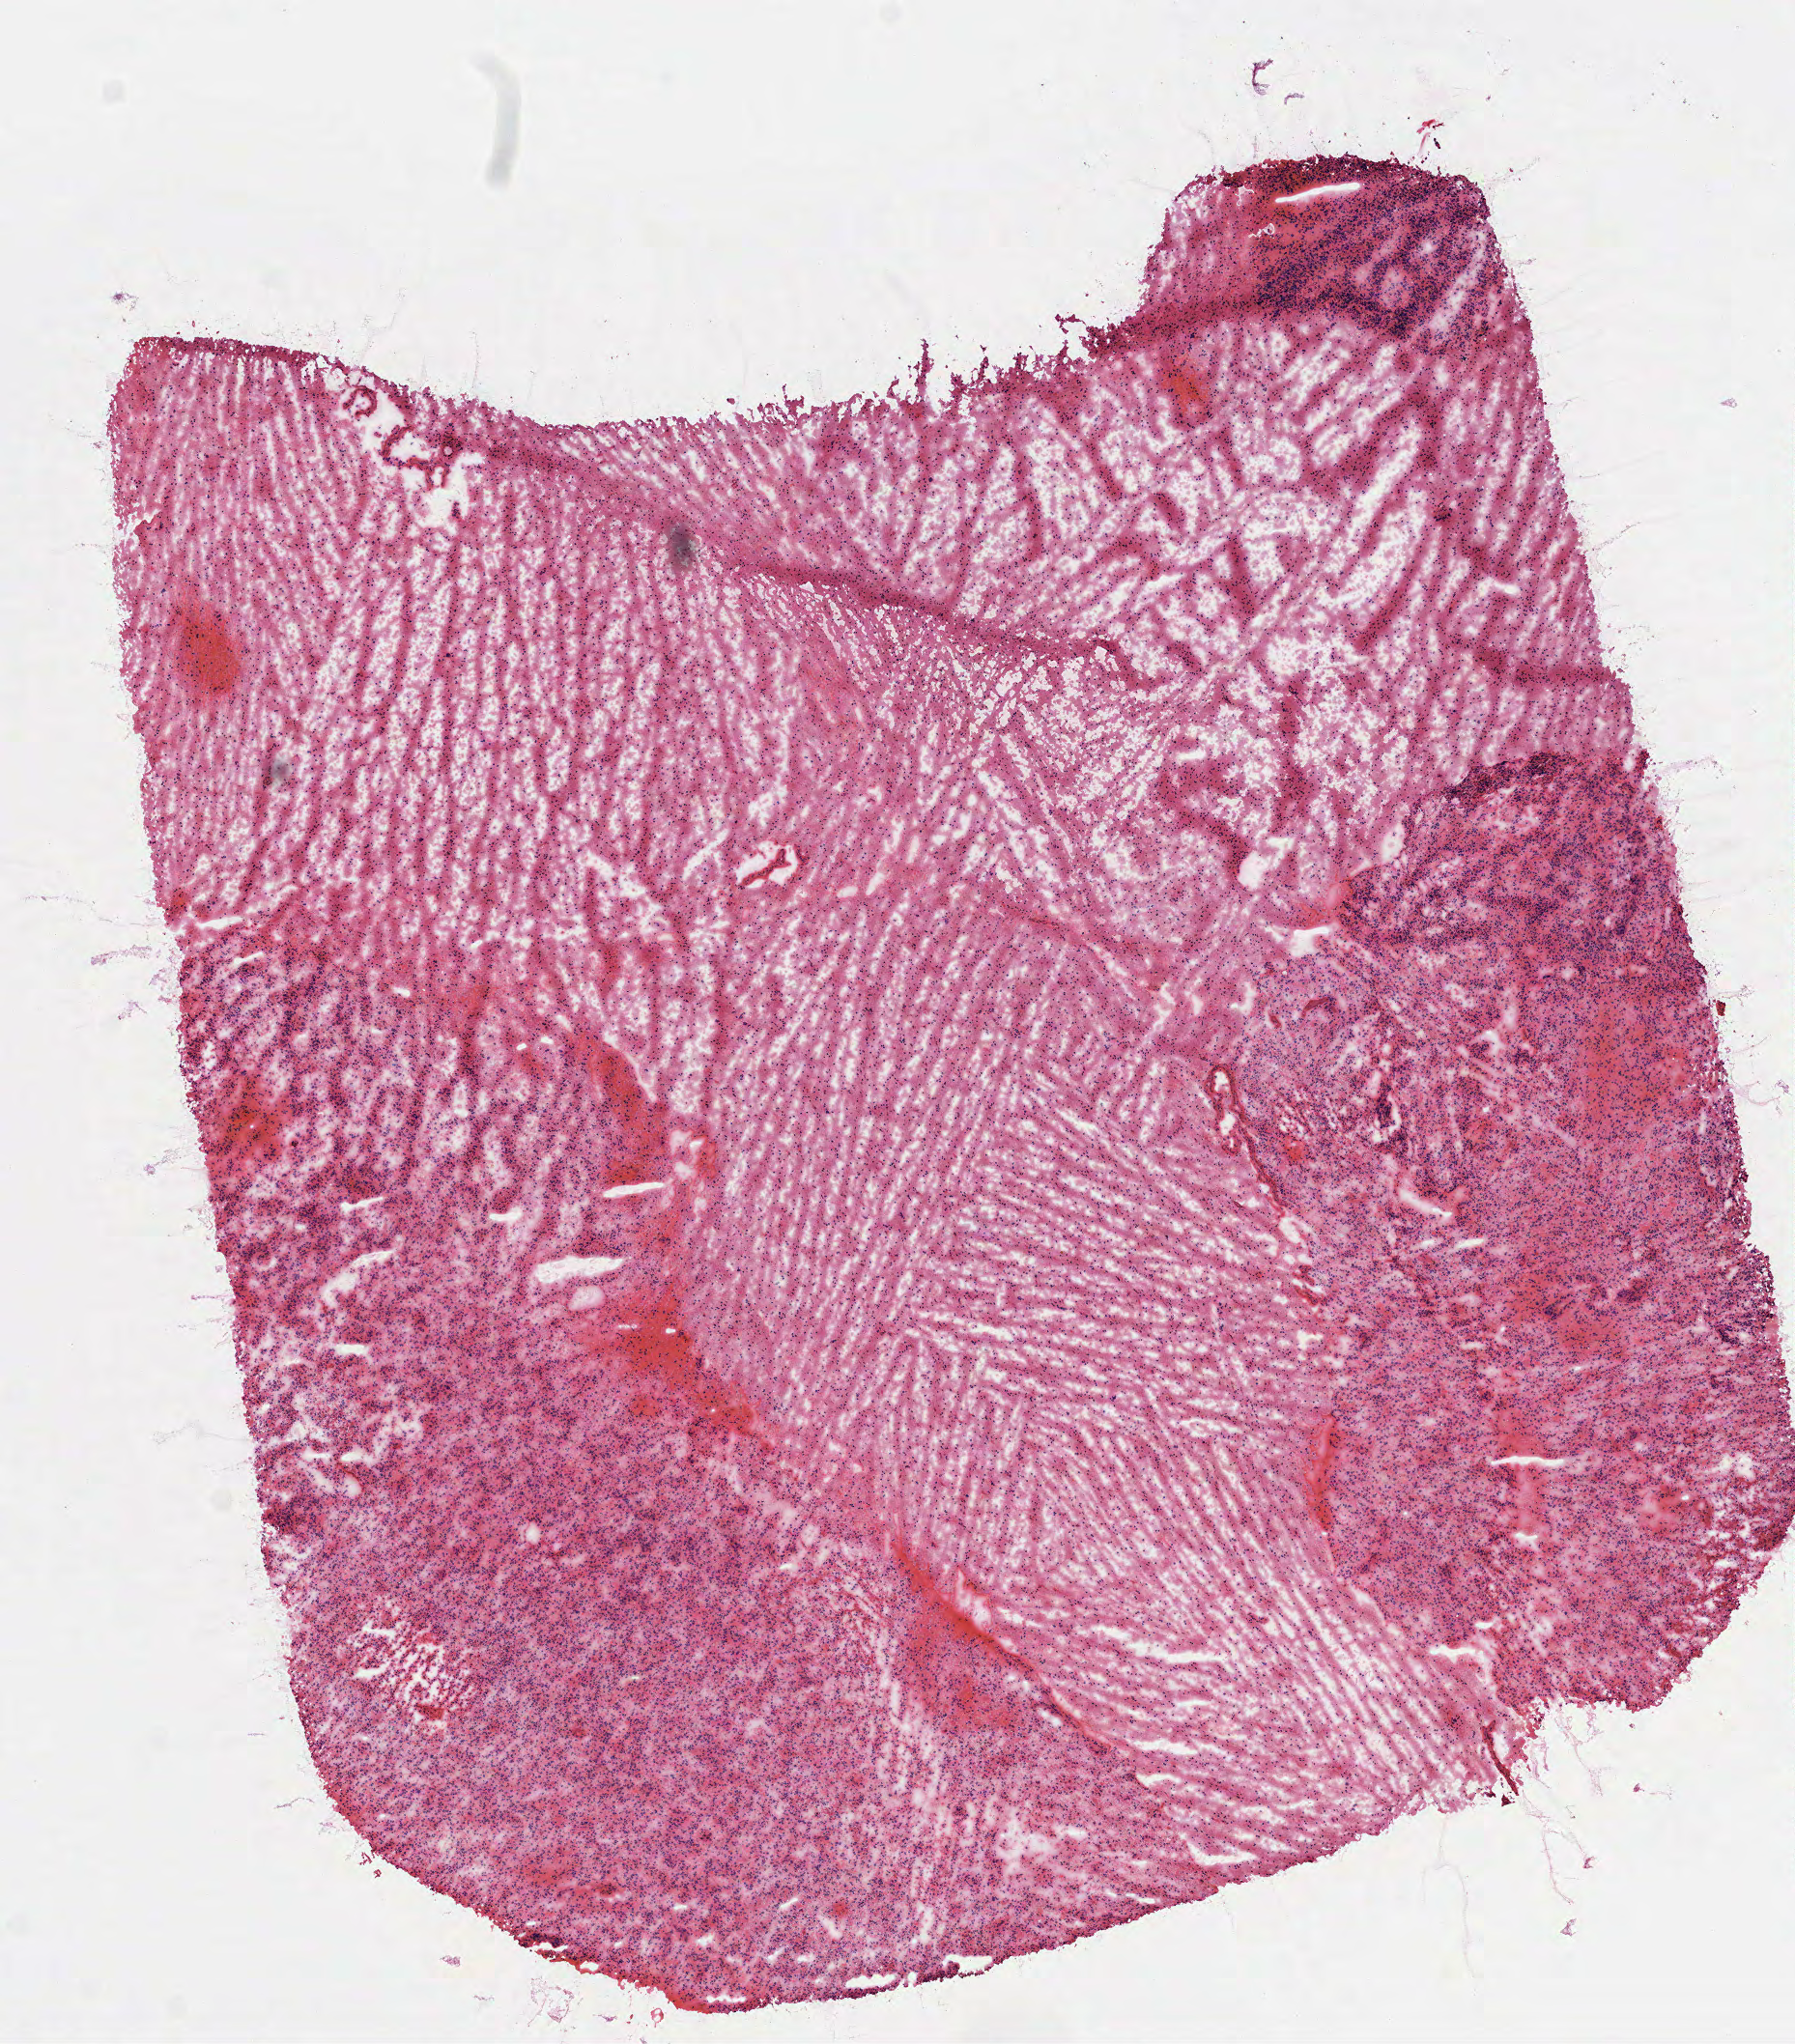
Hematoxylin and eosin (H&E) stained whole-slide image — a low-resolution overview of the entire scanned area, about 7.5 x 8.5 mm (acquisition: 40x scan). Frozen section. Sample: primary tumour, brain. Male, age 78 years at initial diagnosis. Slide review estimates, as recorded: tumour cells 95%, tumour nuclei 80%.
Histologic diagnosis: Glioblastoma.